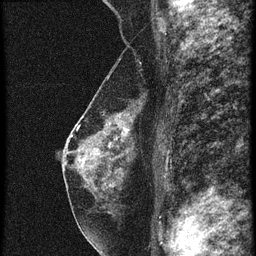
Breast MRI (dynamic contrast-enhanced), one sagittal slice. Position 15 of 28 along the scan axis. 6 images stored at this slice position (order not interpretable as contrast timing). 1.5 T. TE 4.2 ms, TR 20.4 ms. 2.3 mm slice thickness. 256 × 256 image matrix, field of view 180 × 180 mm. Female patient, age 46 years. From the clinical record (not read from this slice): setting: breast cancer imaged before/during neoadjuvant chemotherapy; receptor status: triple-negative.
Outlined on this slice (semi-automatically segmented with operator editing):
- analysis volume of interest (the breast-tissue region the enhancement analysis was run in; not a lesion): bounding box [x1, y1, x2, y2] px = [68, 90, 145, 195]
- tumour enhancement mask (voxels above the 90 % enhancement threshold inside the analysis volume of interest): [124, 118, 131, 133]